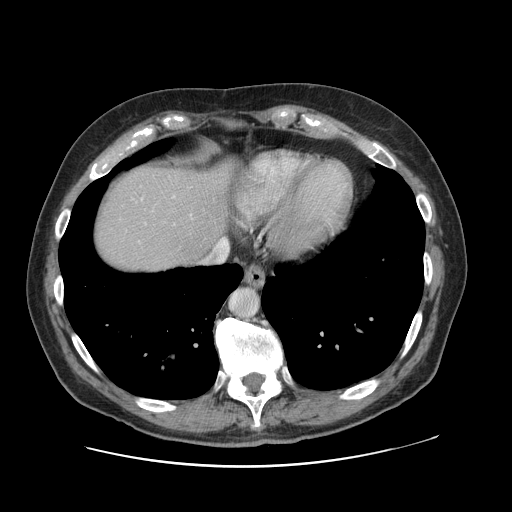
Contrast-enhanced abdominal CT, one axial slice. Position 107 of 138 along the scan axis. 120 kVp. Soft-tissue window (W 400 / L 40 HU). 2.5 mm slice thickness. 512 × 512 image matrix. Male patient, age 71 years. From the clinical record (not read from this slice): diagnosis: colorectal cancer liver metastases, imaged before liver resection; multiple liver metastases: no; largest metastasis: 3.3 cm; disease in both lobes: no.
Structures marked on this image (manually delineated by an expert):
- hepatic veins: box from (x=204, y=238) to (x=229, y=265) px
- liver: (x=93, y=163)–(x=231, y=274)
- planned liver remnant (the part of the liver to remain after resection): (x=94, y=165)–(x=221, y=274)